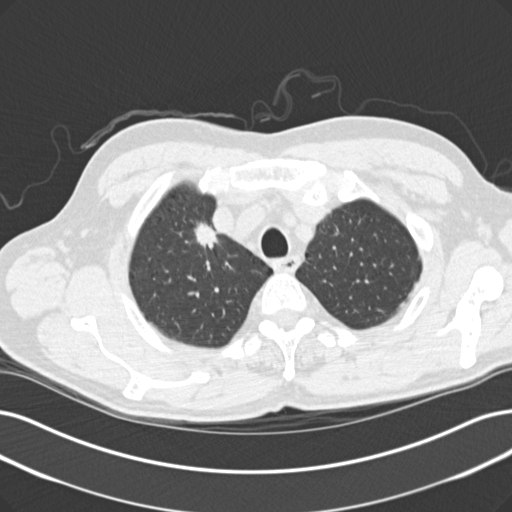
Low-dose screening chest CT, one axial slice; lung window (W 1500 / L -600 HU); 2 mm slice thickness; 512 × 512 image matrix, field of view 365 × 365 mm.
Annotated regions visible in this slice (manually delineated by an expert):
- lesion 1 (tumor, upper lobe of right lung): bounding box <195,223,218,249> (left, top, right, bottom; pixels)